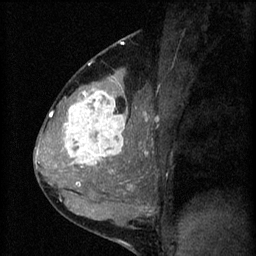
Breast MRI (dynamic contrast-enhanced), one sagittal slice. Position 35 of 60 along the scan axis. 3 images stored at this slice position (order not interpretable as contrast timing). 1.5 T. TE 4.2 ms, TR 8.2 ms. 2 mm slice thickness. 256 × 256 image matrix, field of view 180 × 180 mm. Patient: female, 37 years.
Outlined on this slice (semi-automatic segmentation, software-assisted and operator-edited):
- analysis volume of interest (the breast-tissue region the enhancement analysis was run in; not a lesion): bounding box (x1, y1, x2, y2) in pixels: (53, 78, 140, 181)
- tumour enhancement mask (voxels above the 70 % enhancement threshold inside the analysis volume of interest): (62, 90, 126, 171)